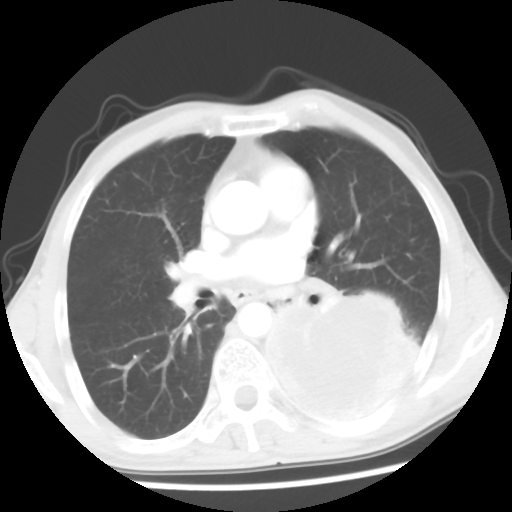
Chest CT, one axial slice; slice 30 of 56 in the series (ordered by position); reconstruction kernel STANDARD; lung window (W 1500 / L -600 HU); 512 × 512 image matrix. Patient: male, 60 years. From the clinical record (not read from this slice): clinical TNM (as recorded): T4 N0 M0.
Outlined on this slice (bounding box drawn by a radiologist):
- lung tumour (recorded histology: squamous cell carcinoma): bounding box <260,275,425,420> (left, top, right, bottom; pixels)